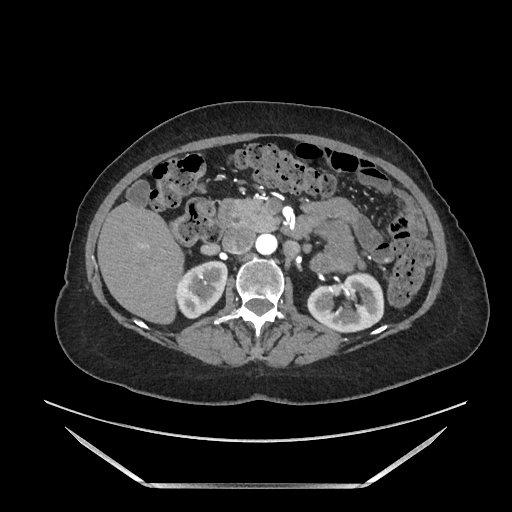
Contrast-enhanced abdominal CT, one axial slice; position 85 of 205 along the scan axis; soft-tissue window (W 400 / L 40 HU); 512 × 512 image matrix, field of view 440 × 440 mm. Female patient. From the clinical record (not read from this slice): diagnosis: adrenocortical carcinoma; tumour side: left adrenal; tumour size at pathology: 12.5 cm; Ki-67 index: 39 %; stage (as recorded): 3.
Outlined on this slice (semi-automatically segmented with operator editing):
- mass: box from (x=313, y=224) to (x=357, y=273) px